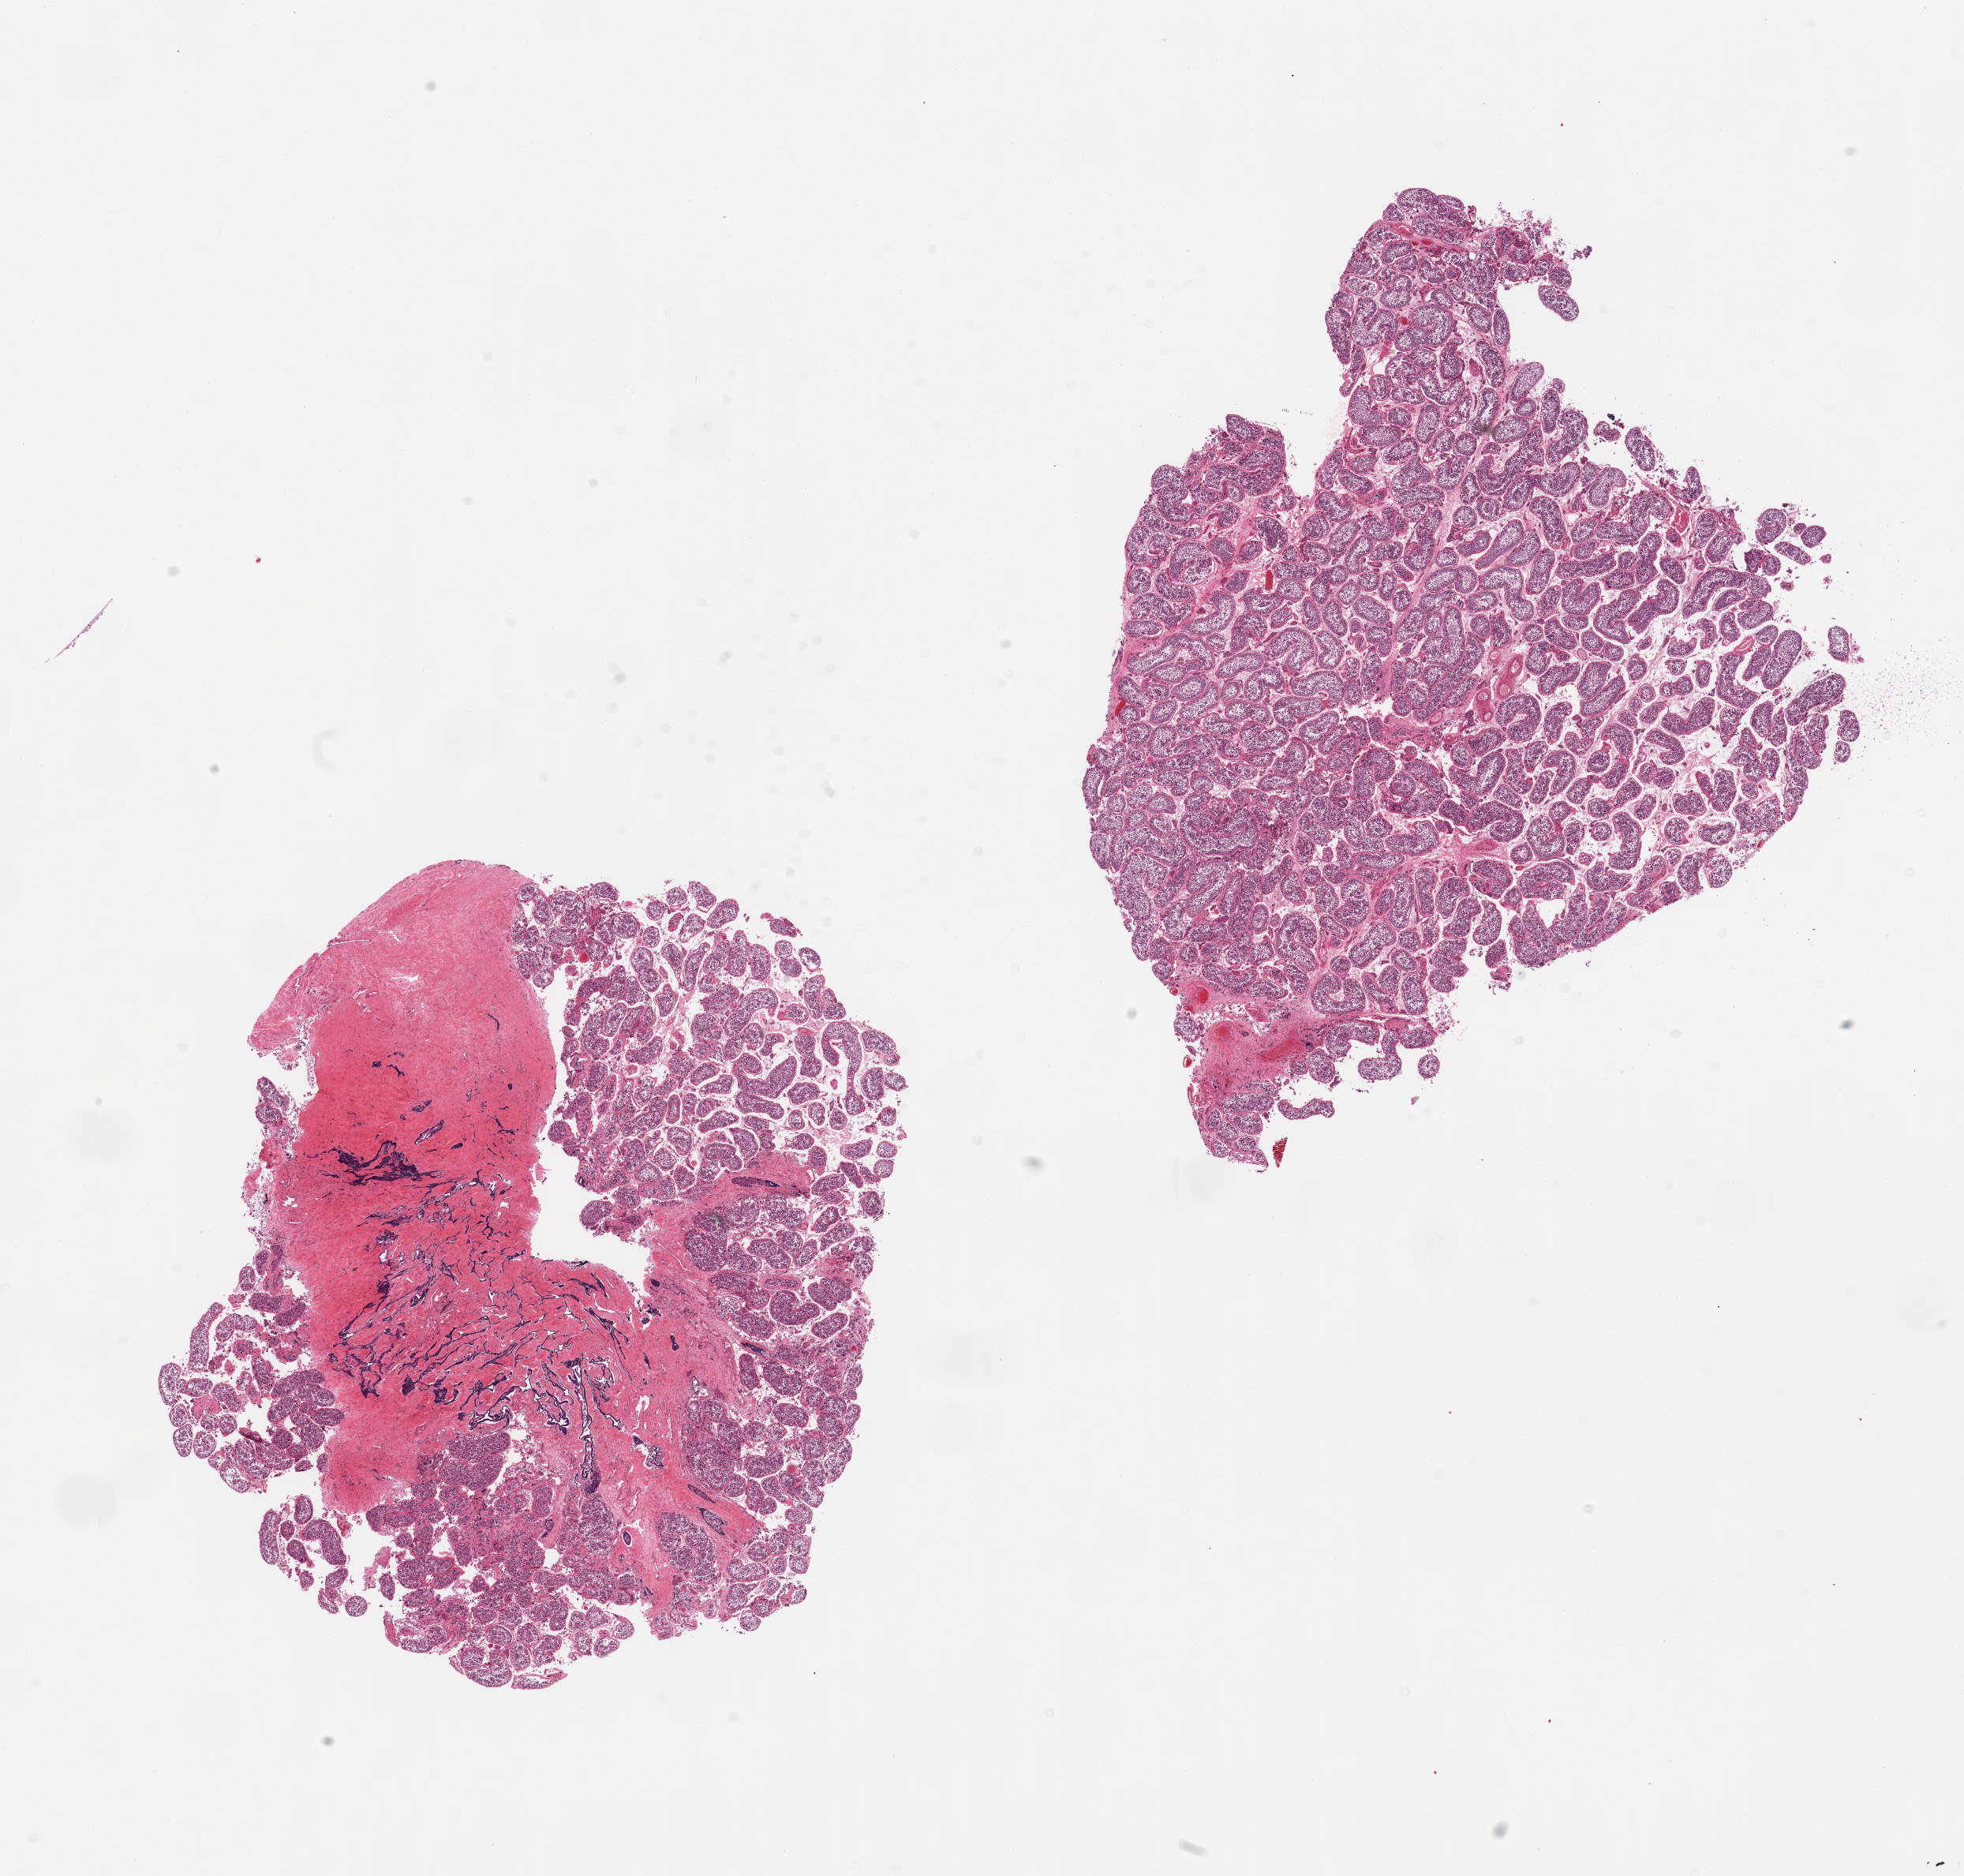
Whole-slide image, H&E stain — whole scanned area (about 19.7 x 18.8 mm, from a 20x scan) shown as a low-resolution overview. PAXgene-fixed, paraffin-embedded tissue. Target tissue: testis. Donor tissue sample.
Reviewer comment on this tissue sample: 2 pieces, active spermatogenesis, rete testis.